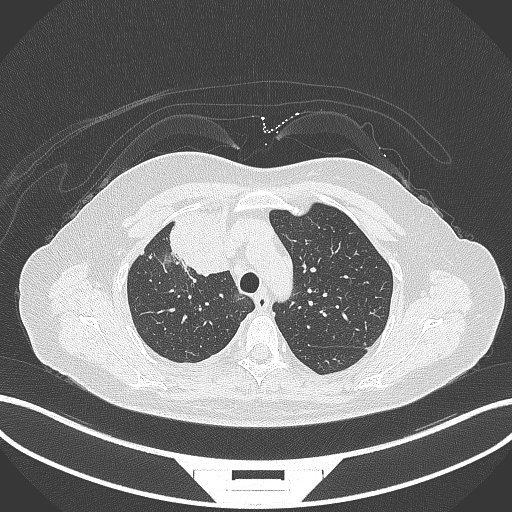
Chest CT, one axial slice; position 229 of 305 along the scan axis; lung window (W 1500 / L -600 HU); 512 × 512 image matrix, field of view 400 × 400 mm. Patient: female, 52 years. From the clinical record (not read from this slice): clinical TNM (as recorded): T3 N1 M1.
Annotated regions visible in this slice (rectangle marked by the reading radiologist):
- lung tumour (recorded histology: adenocarcinoma): bounding box [x1, y1, x2, y2] px = [167, 212, 229, 278]